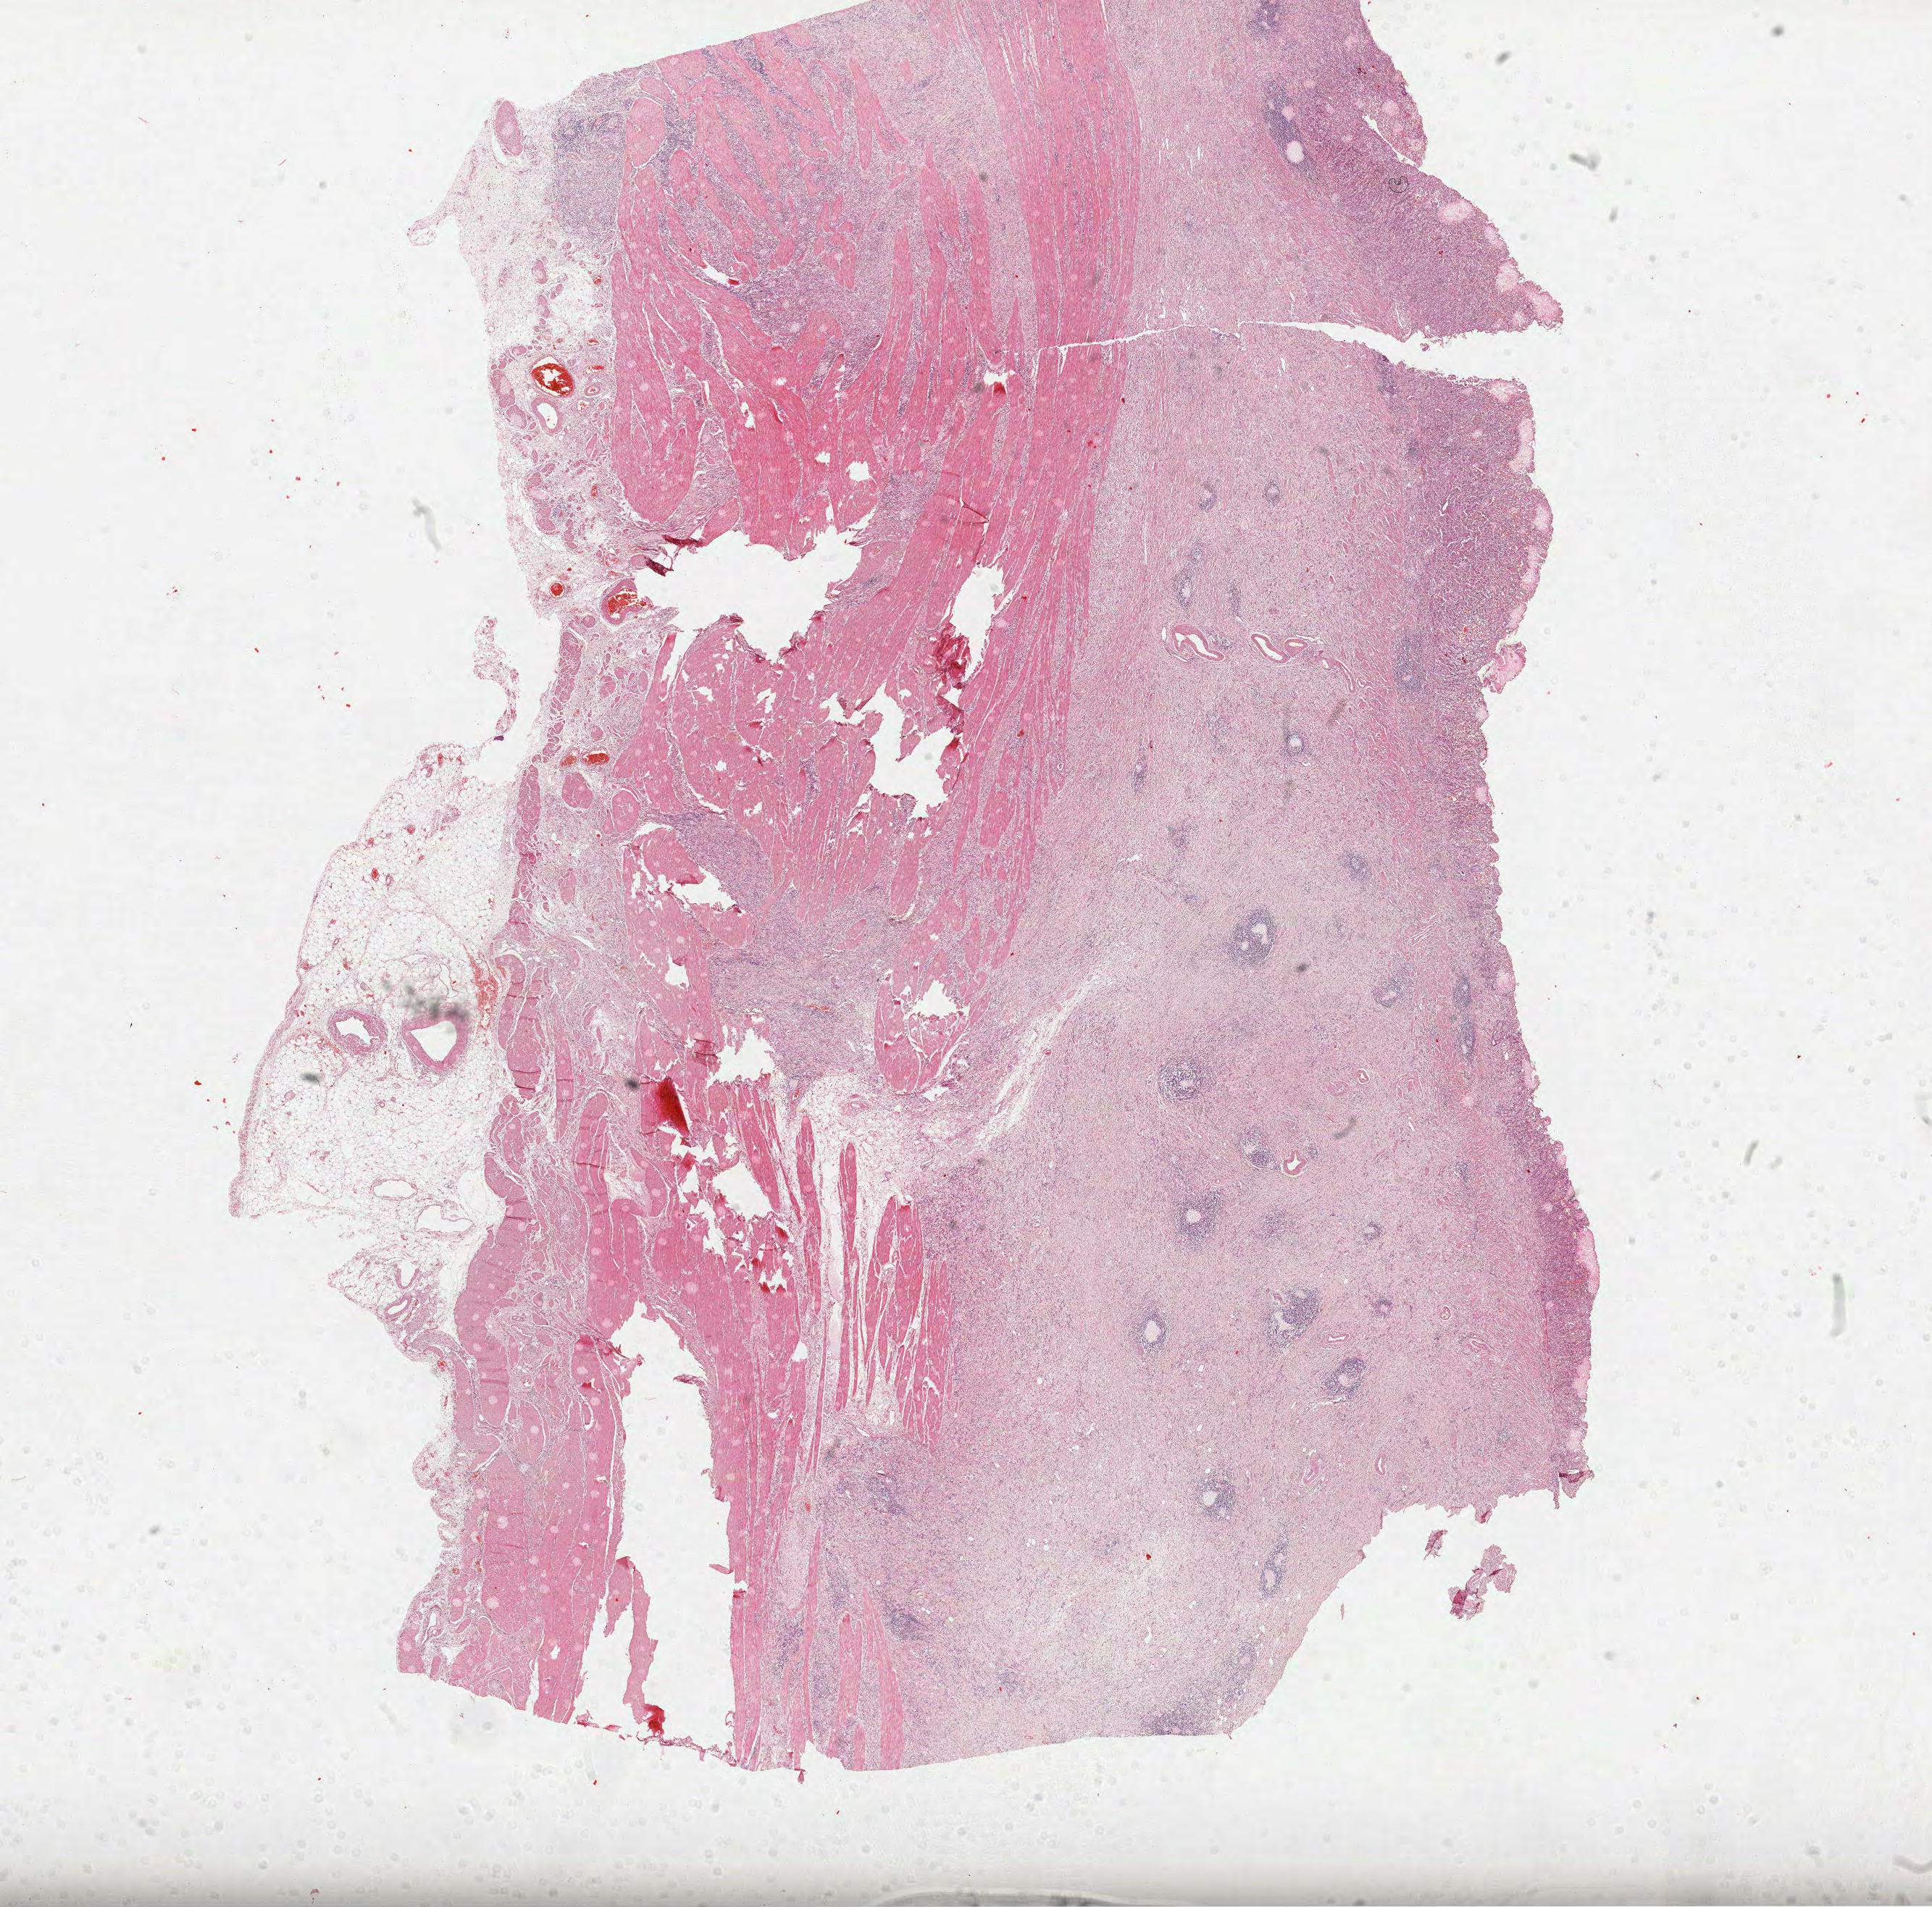
Digitized H&E tissue section (whole slide) — a low-resolution overview of the entire scanned area, about 21.5 x 21.2 mm (acquisition: 40x scan); FFPE section; primary tumour sample from the stomach. Patient: male, age at initial diagnosis 53 years. Histologic grade: G3 (poorly differentiated).
Lymph nodes positive (case pathology): 6 of 16 examined. Diagnosis: Carcinoma, diffuse type (gastric antrum). AJCC pathologic stage: II (6th edition).